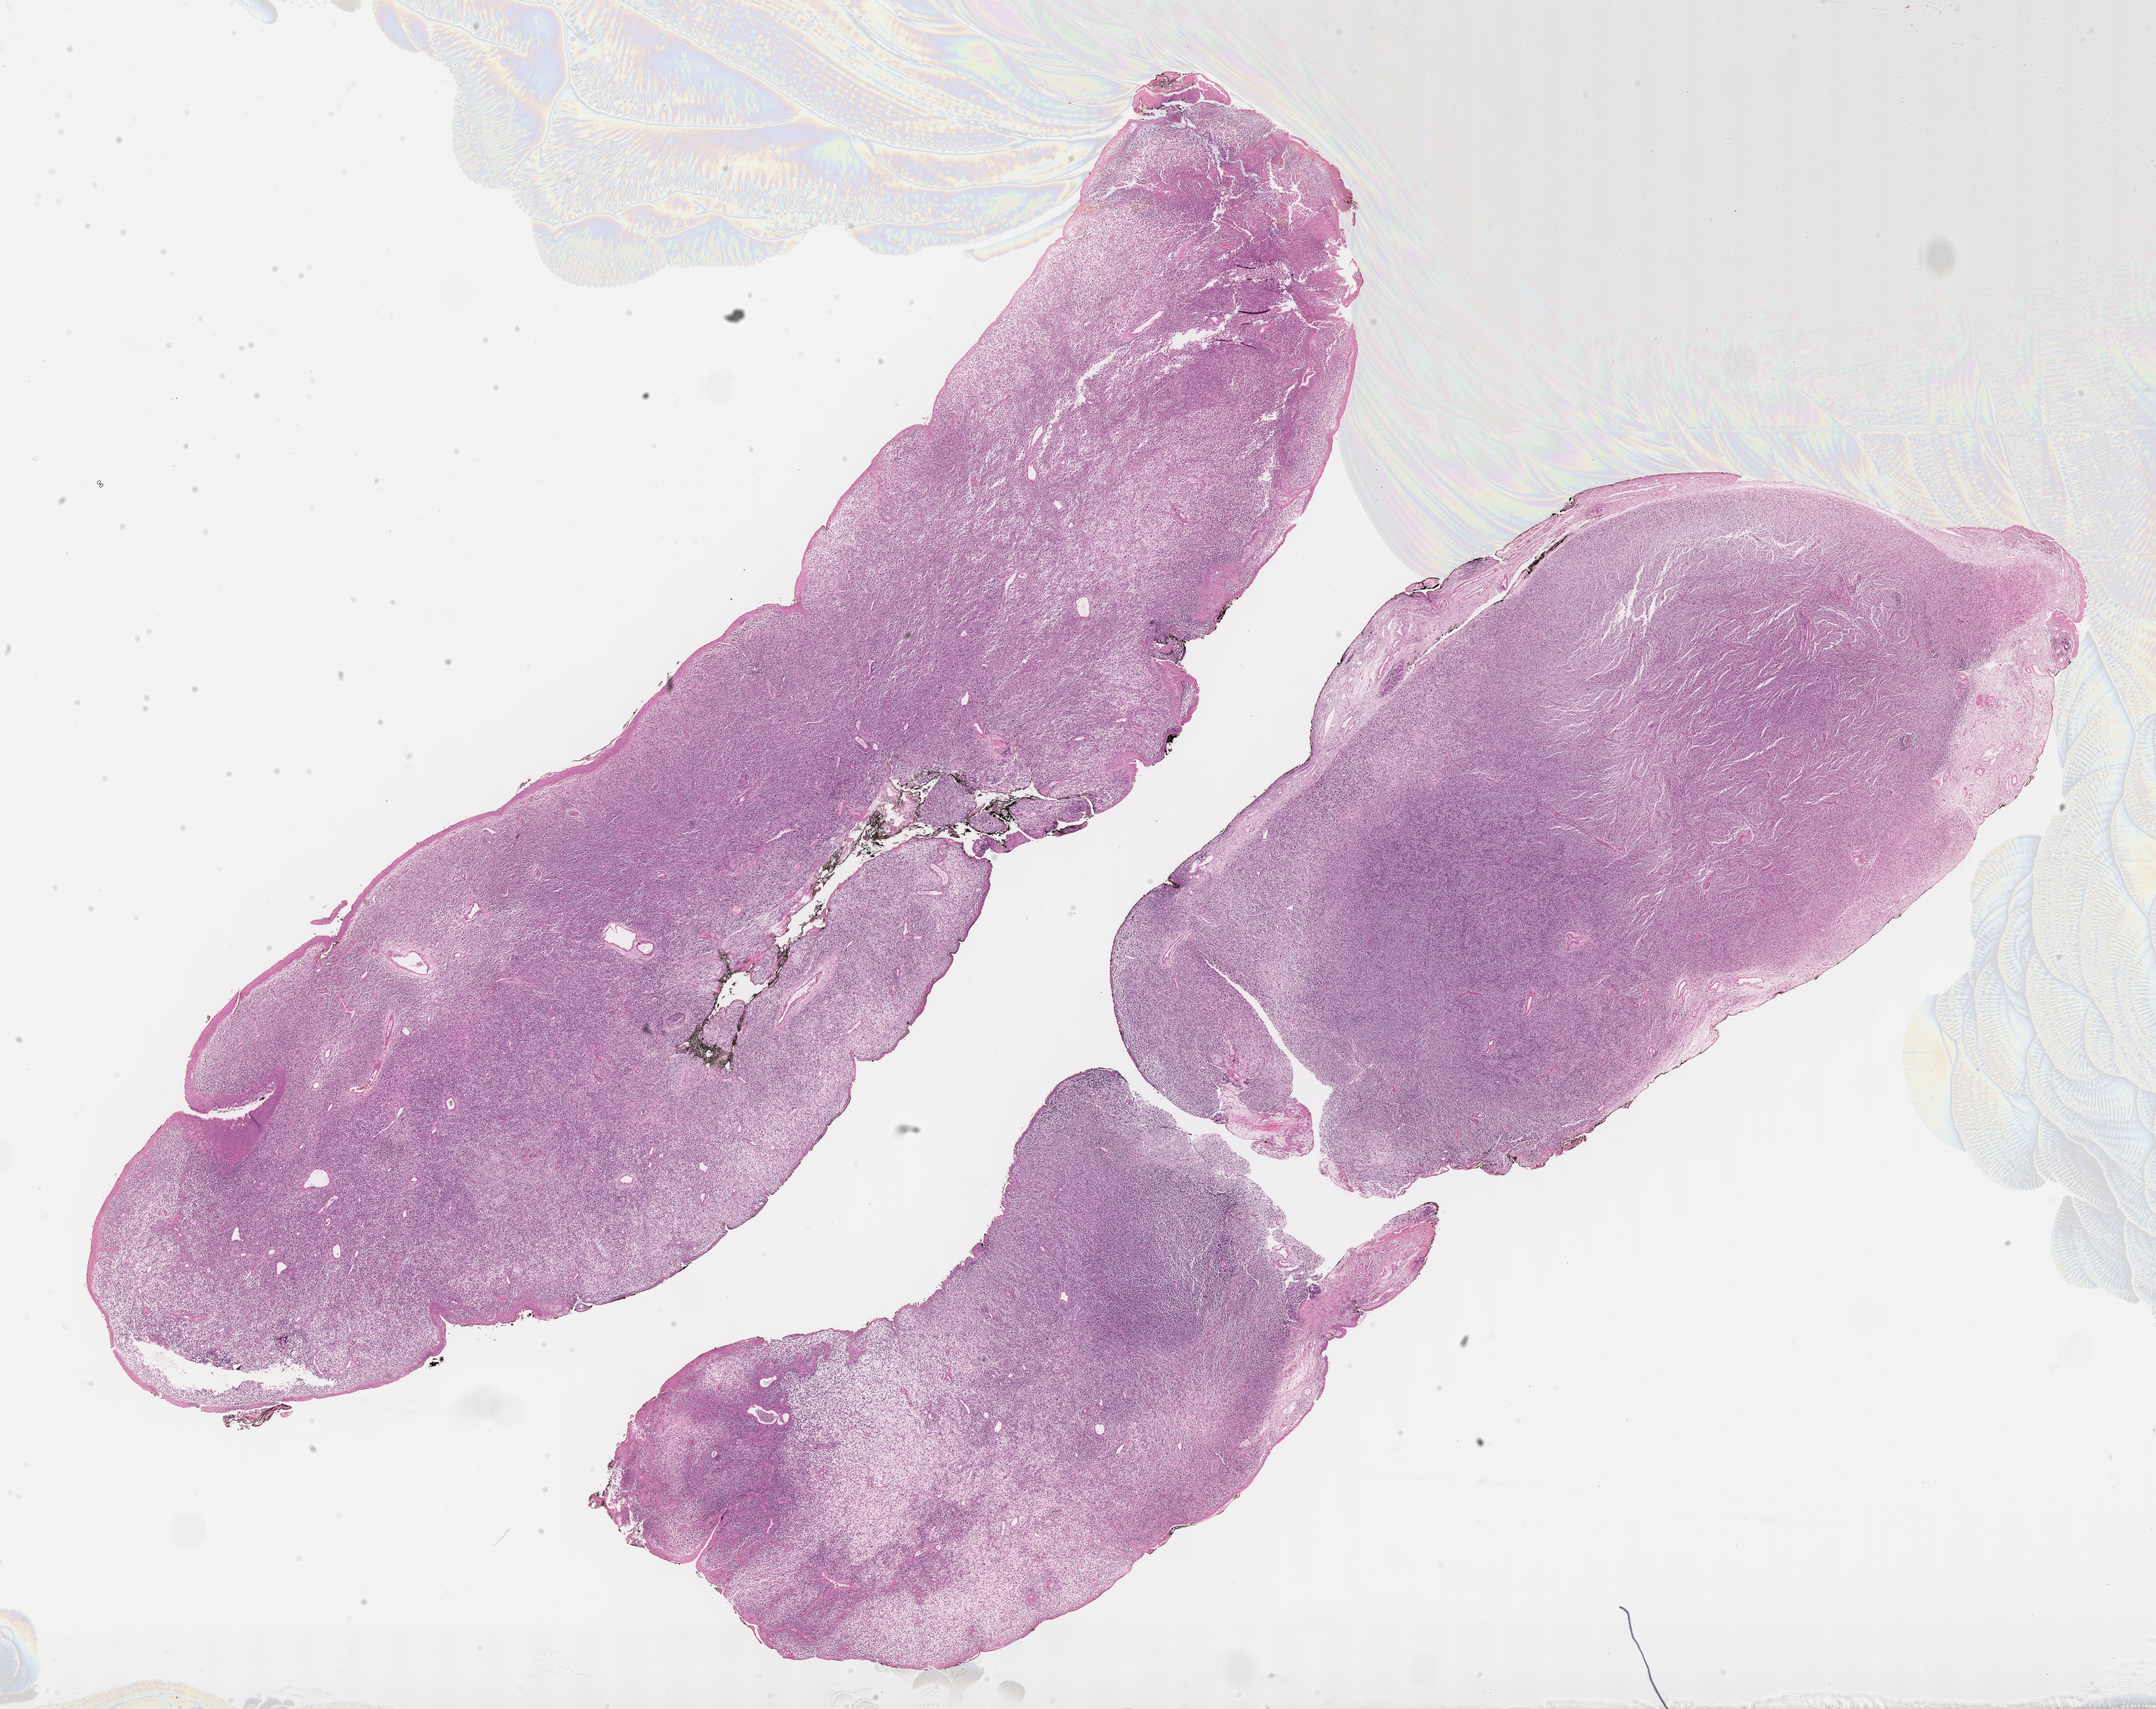
Hematoxylin and eosin (H&E) whole-slide image of tumor tissue, whole scanned area (about 23.1 x 18.4 mm) shown as a low-resolution overview. Formalin-fixed, paraffin-embedded (FFPE) tissue. Site: eye, orbit-left. Male patient, age at diagnosis 5.7 years.
Diagnosis: rhabdomyosarcoma; histological classification: embryonal rhabdomyosarcoma. Metastatic status at presentation (as recorded): non-metastatic. Stage (as recorded): 1.